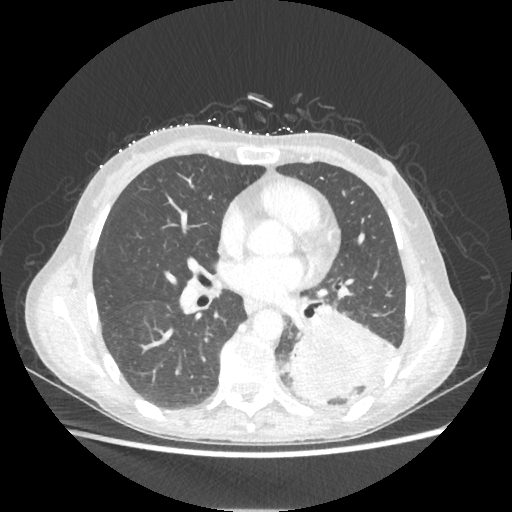
Chest CT, one axial slice; position 110 of 221 along the scan axis; 80 kVp; lung window (W 1500 / L -600 HU); 1.25 mm slice thickness; 512 × 512 image matrix, field of view 360 × 360 mm. Female patient, age 53 years. Case-level facts recorded for this patient, not image findings: clinical TNM (as recorded): T3 N0 M0.
Outlined on this slice (rectangle marked by the reading radiologist):
- lung tumour (recorded histology: adenocarcinoma): bounding box [x1, y1, x2, y2] px = [283, 303, 397, 405]